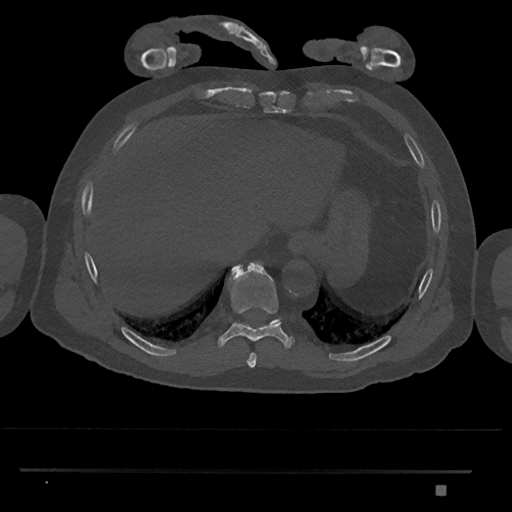
CT including the spine, one axial slice. Reconstruction kernel Br40s/3. 120 kVp. Bone window (W 1800 / L 400 HU). 0.5 mm slice thickness. 512 × 512 image matrix, field of view 429 × 429 mm. Patient: male, 65 years. From the clinical record (not read from this slice): primary cancer: prostate.
Structures marked on this image (semi-automatic segmentation, software-assisted and operator-edited):
- T10 vertebra: box from (x=236, y=318) to (x=281, y=324) px
- T8 vertebra: (x=246, y=353)–(x=257, y=367)
- T9 vertebra: (x=218, y=262)–(x=295, y=348)